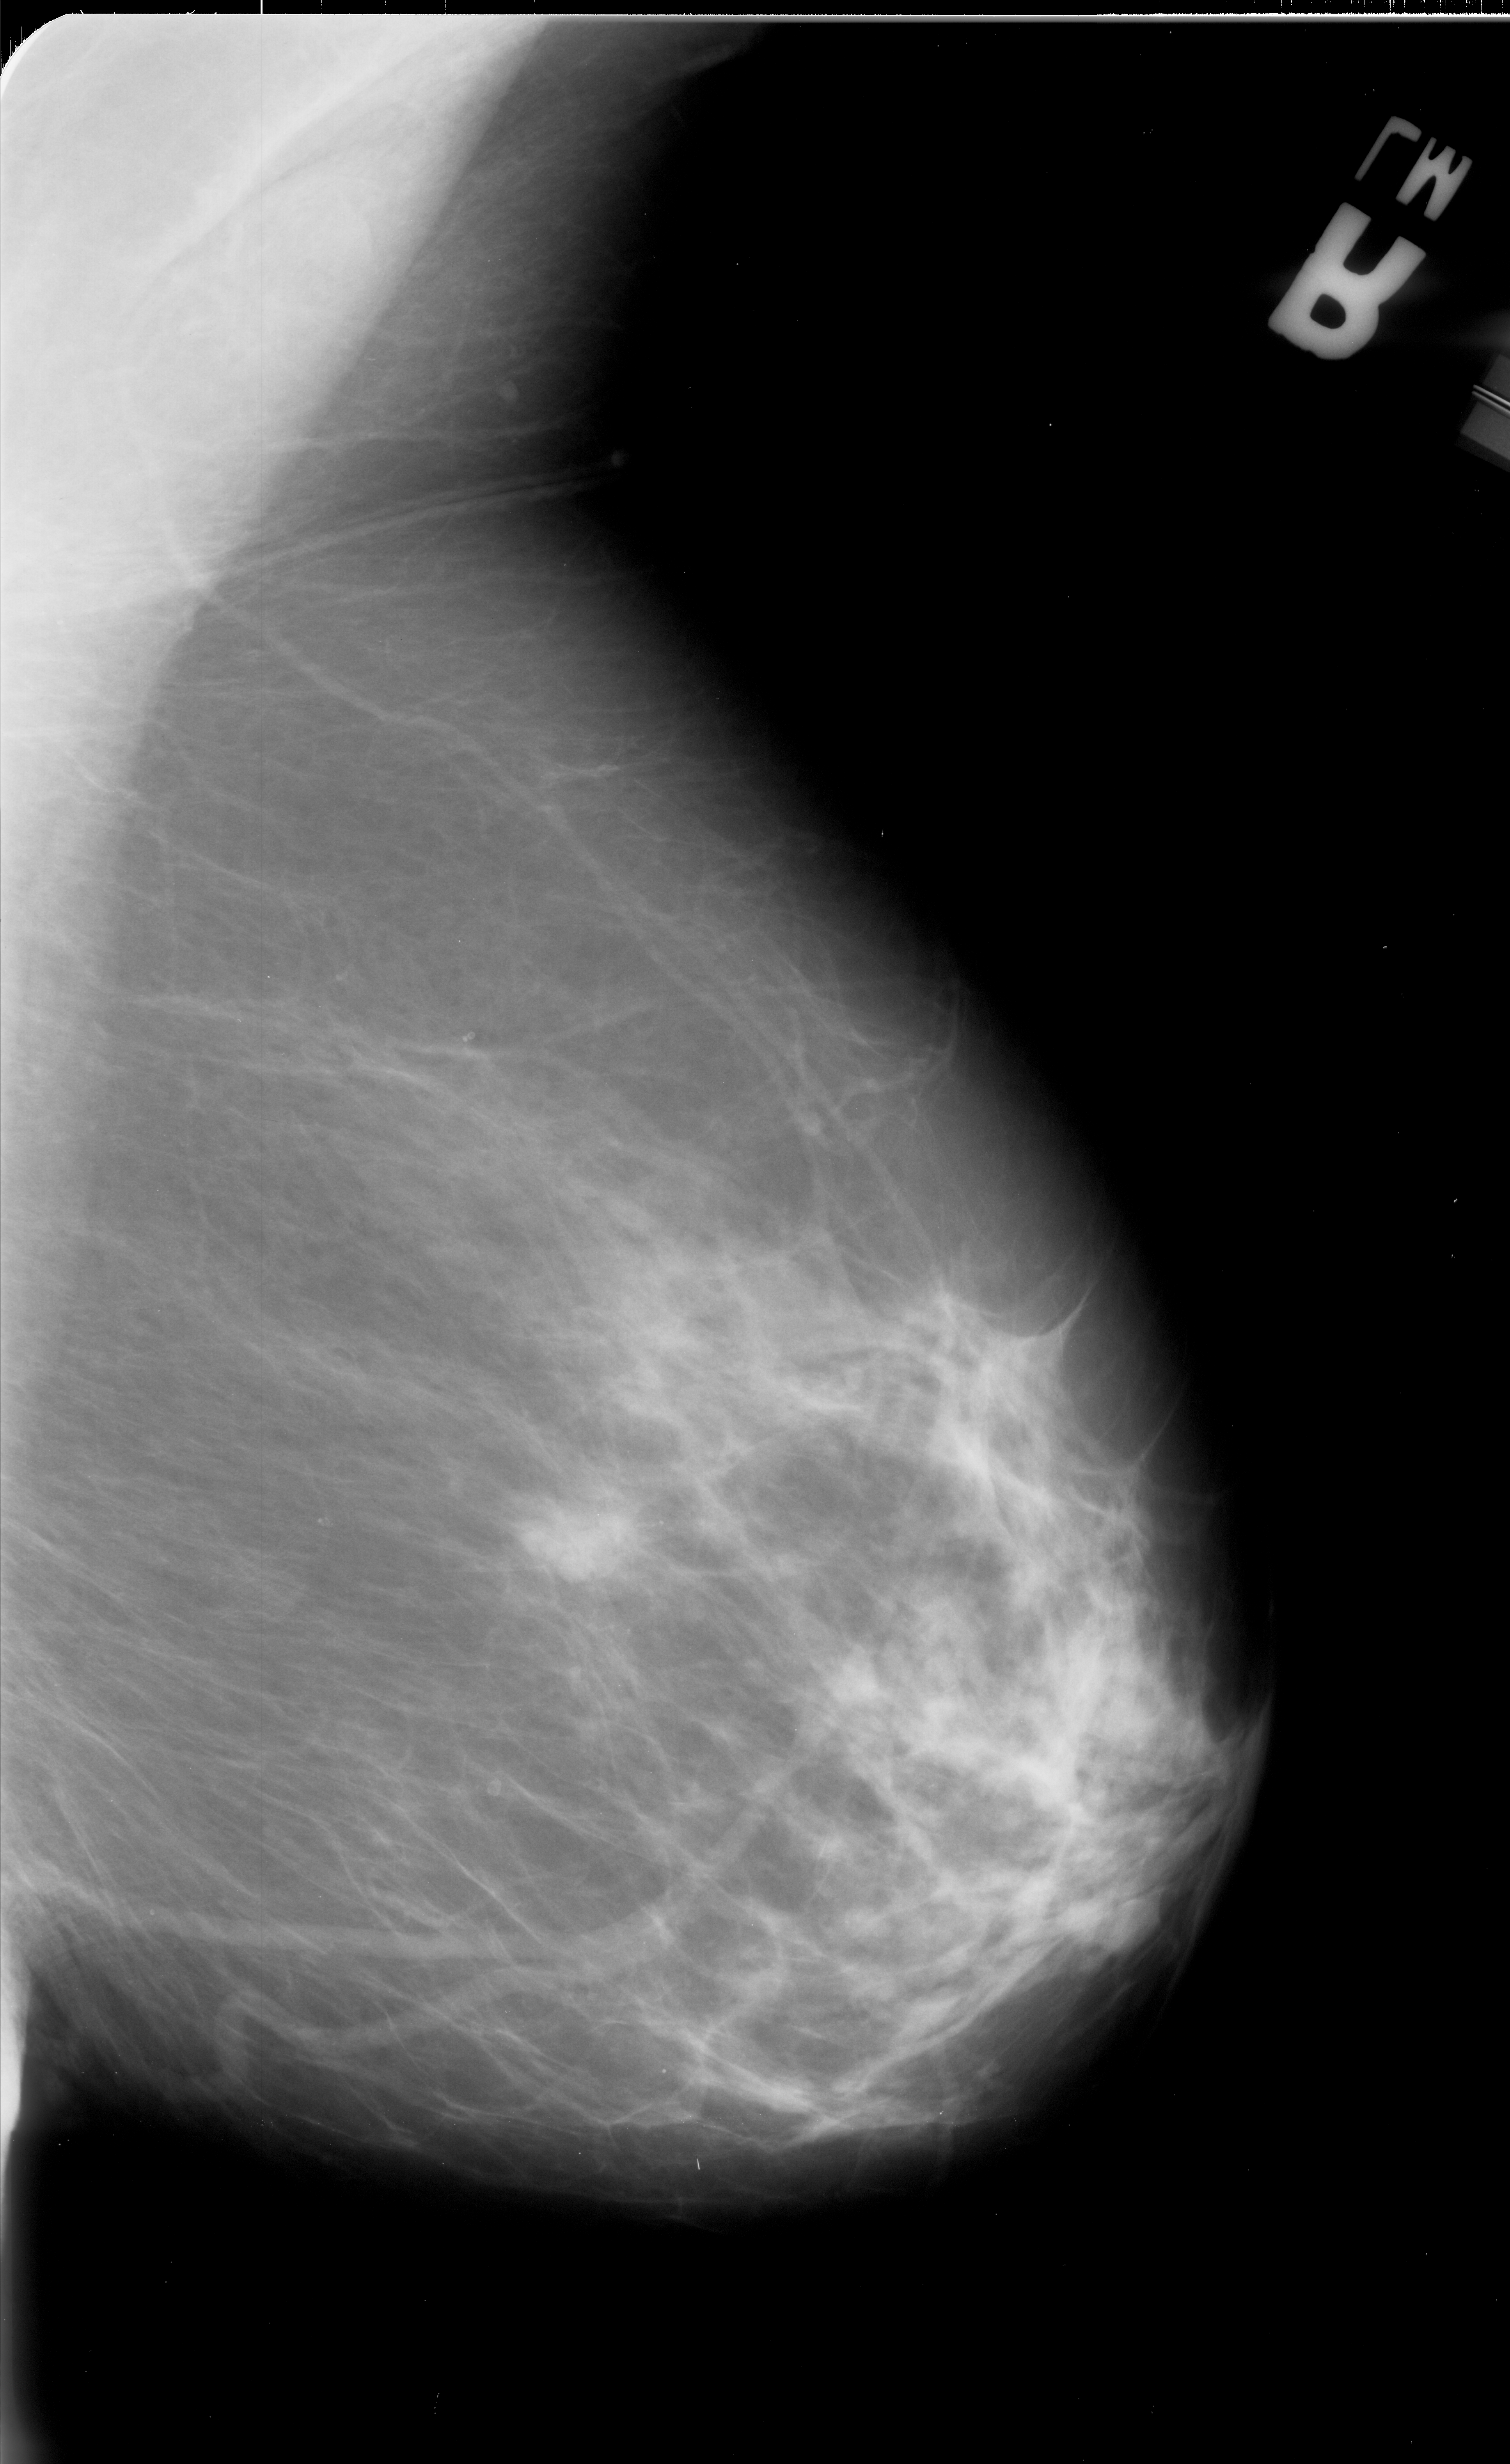
Mammogram (digitized film). Right breast. Mediolateral oblique (MLO) view. Breast composition: scattered fibroglandular densities (BI-RADS density category 2 of 4). 1510 × 2464 image matrix.
Expert-marked regions of interest on this film, with their recorded descriptors:
- mass, shape lobulated, margins spiculated; BI-RADS assessment category 5; pathology (as recorded): malignant: bounding box (x1, y1, x2, y2) in pixels: (502, 1466, 642, 1585)